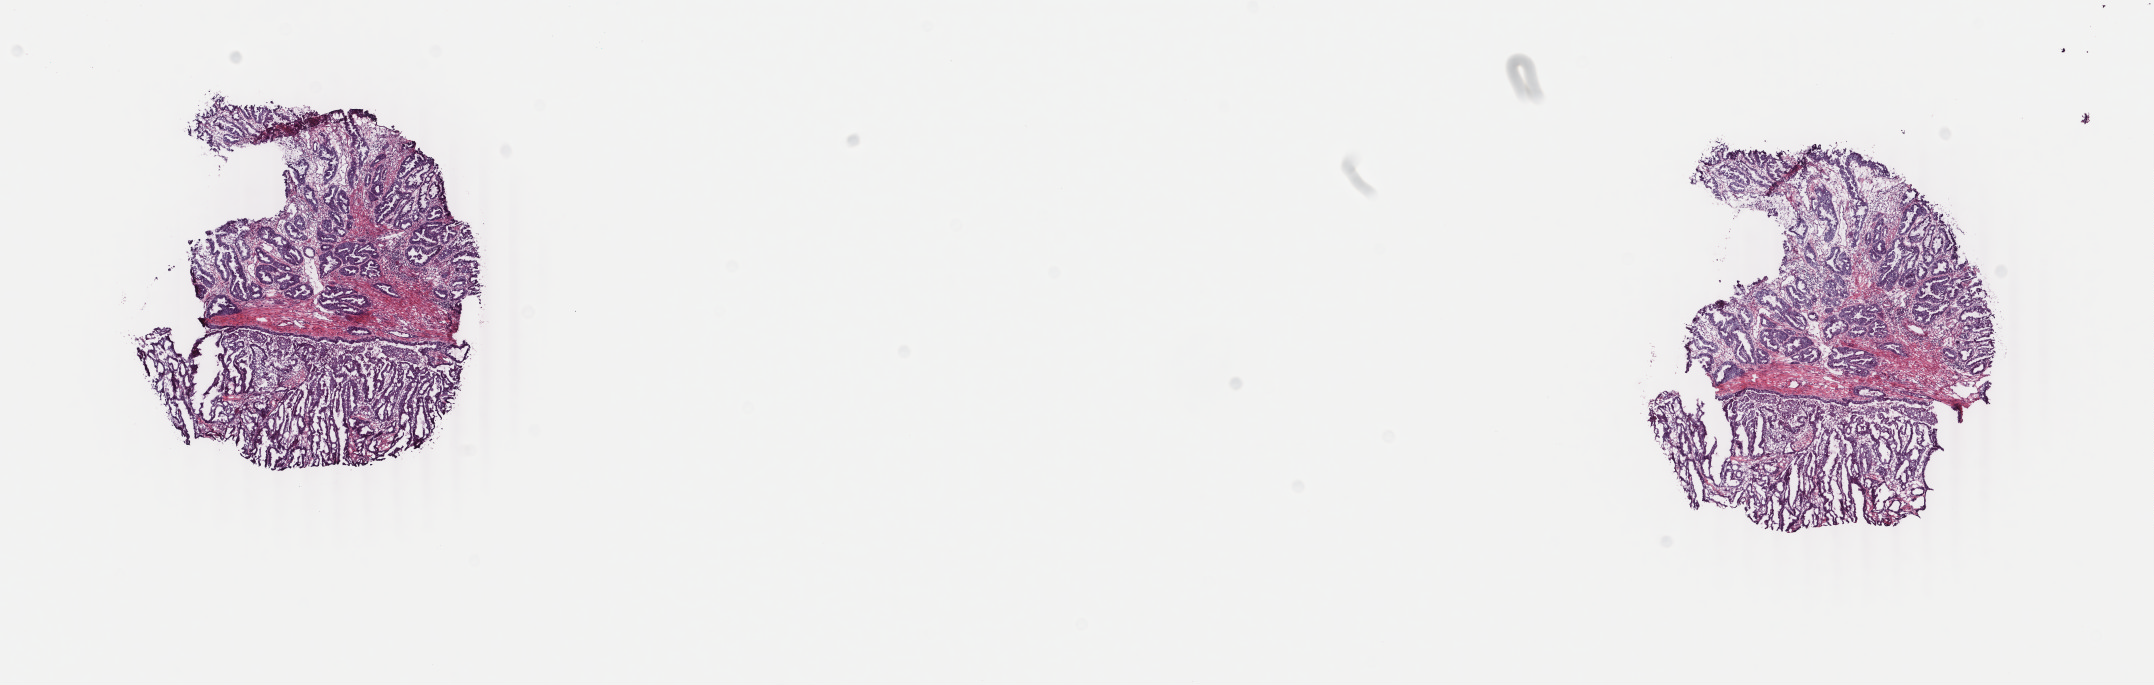
Whole-slide histology image, H&E, whole scanned area (about 17.1 x 5.4 mm) shown as a low-resolution overview, frozen section from the top of the tissue portion, primary tumour sample from the esophagus. Patient: male, age at initial diagnosis 53 years. Histologic grade: G2 (moderately differentiated). Pathologist review of this section (percent, as recorded): tumour cells 85%, tumour nuclei 85%, normal cells 0%, stromal cells 15%, necrosis 0%. Infiltration values recorded for this section: lymphocyte infiltration 4%, monocyte infiltration 2%, neutrophil infiltration 1%.
Lymph nodes positive (case pathology): 2 of 18 examined. AJCC pathologic stage: IIB (7th edition). Pathologic diagnosis: Adenocarcinoma, NOS (lower third of esophagus).